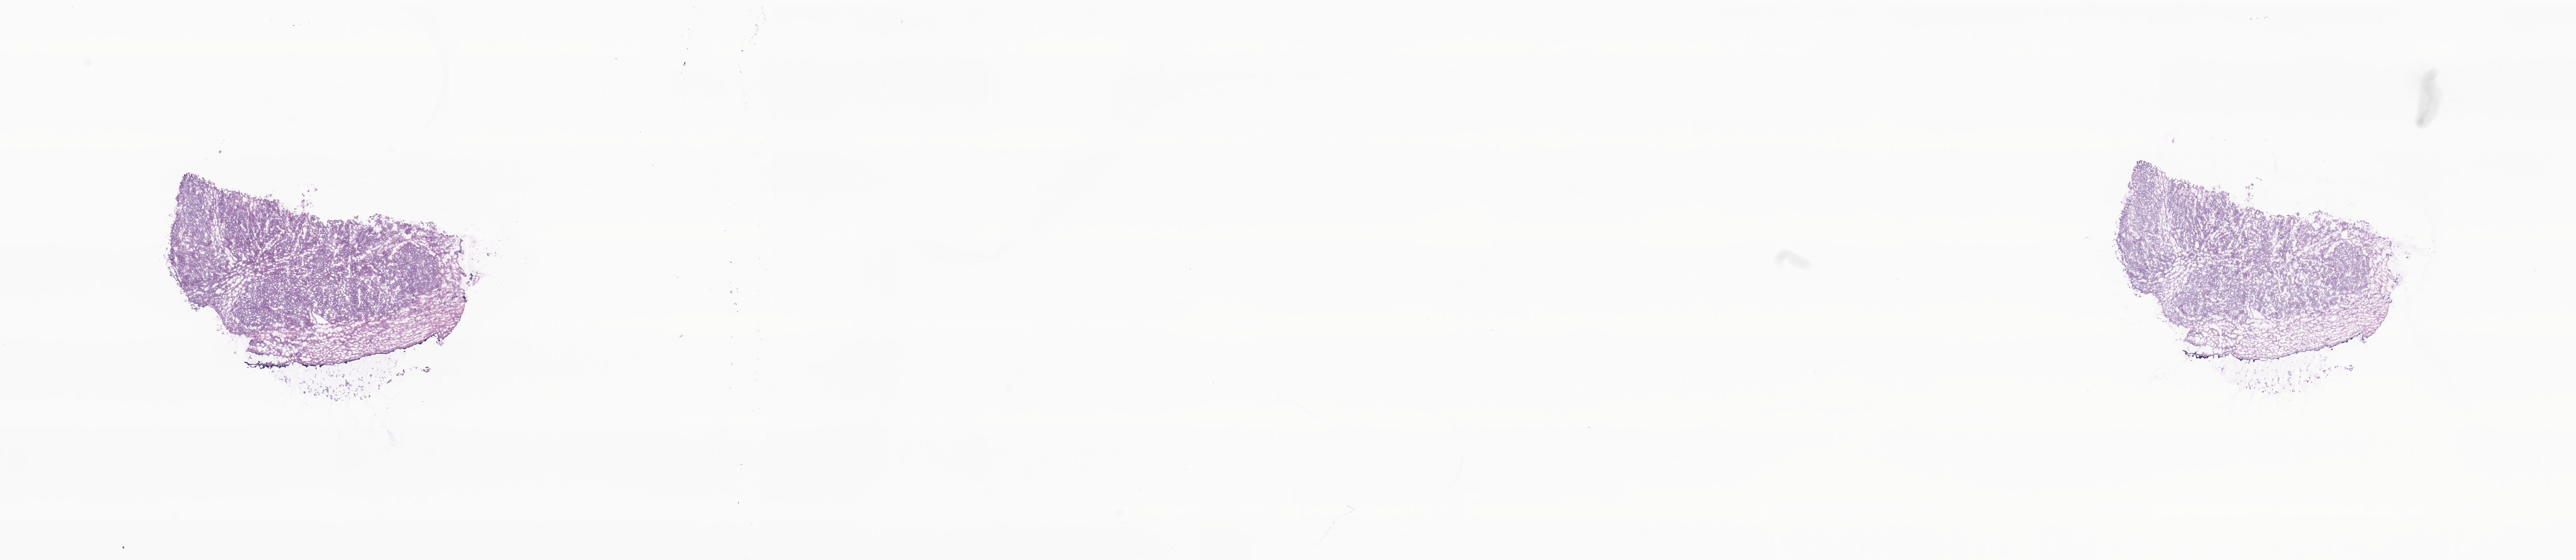
Whole-slide image, haematoxylin and eosin stain, a low-resolution overview of the entire scanned area, about 29.7 x 6.5 mm, frozen section (tissue freezing medium), specimen: metastatic tumor tissue. Patient sex: female. Pathologist review of this section (percent, as recorded): tumor cells 75%, tumor nuclei 87%.
Patient diagnosis (primary): Serous surface papillary carcinoma.